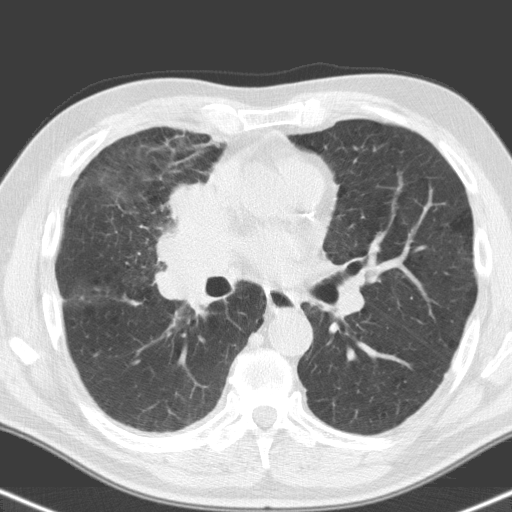
Low-dose screening chest CT, one axial slice. Position 88 of 160 along the scan axis. 120 kVp. Lung window (W 1500 / L -600 HU). 3.2 mm slice thickness. 512 × 512 image matrix, field of view 324 × 324 mm.
Annotated regions visible in this slice (manually delineated by an expert):
- lesion 1 (tumor, hilum of right lung): box from (x=158, y=185) to (x=242, y=308) px